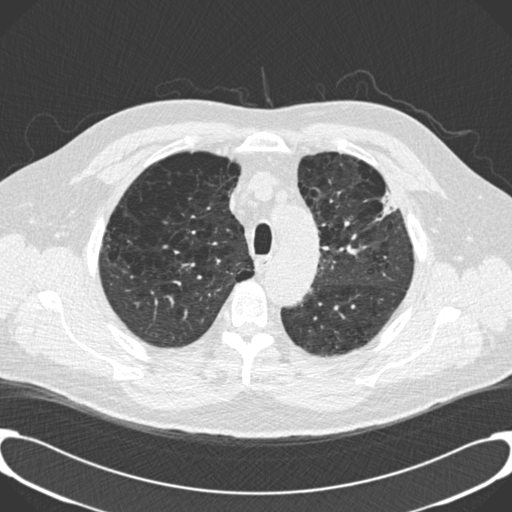
Axial slice from a low-dose chest CT screening exam, third screening round (two years after baseline), lung window (W 1500 / L -600 HU), 2 mm slice thickness, standard (soft-tissue) reconstruction kernel (B30f), 120 kVp, slice 36 of 189 in the series, 512 × 512 image matrix. Male, age 59 years at enrolment. Current smoker at enrolment.
• Expert-annotated lung lesion, box from (x=363, y=173) to (x=411, y=229) px.
• No non-calcified nodule or mass ≥4 mm was recorded by the screening reader at this exam.
• Official screen result: positive, other.
• Participant outcome: lung cancer diagnosed 134 days after this screen — bronchiolo-alveolar carcinoma, mixed mucinous and non-mucinous, left upper lobe, stage IA (AJCC 6th edition), 20 mm at pathology.